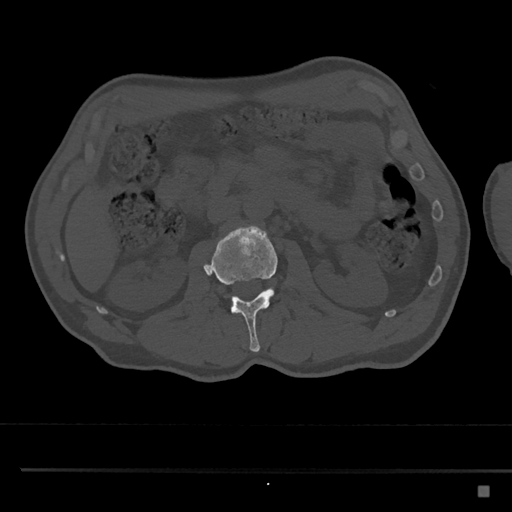
CT including the spine, one axial slice; slice 750 of 797 in the series (ordered by position); reconstruction kernel Br40s/3; bone window (W 1800 / L 400 HU); 512 × 512 image matrix, field of view 391 × 391 mm. Male patient, age 59 years. Case-level facts recorded for this patient, not image findings: primary cancer: prostate.
Structures marked on this image (semi-automatically segmented with operator editing):
- L2 vertebra: bounding box [x1, y1, x2, y2] px = [203, 226, 278, 352]